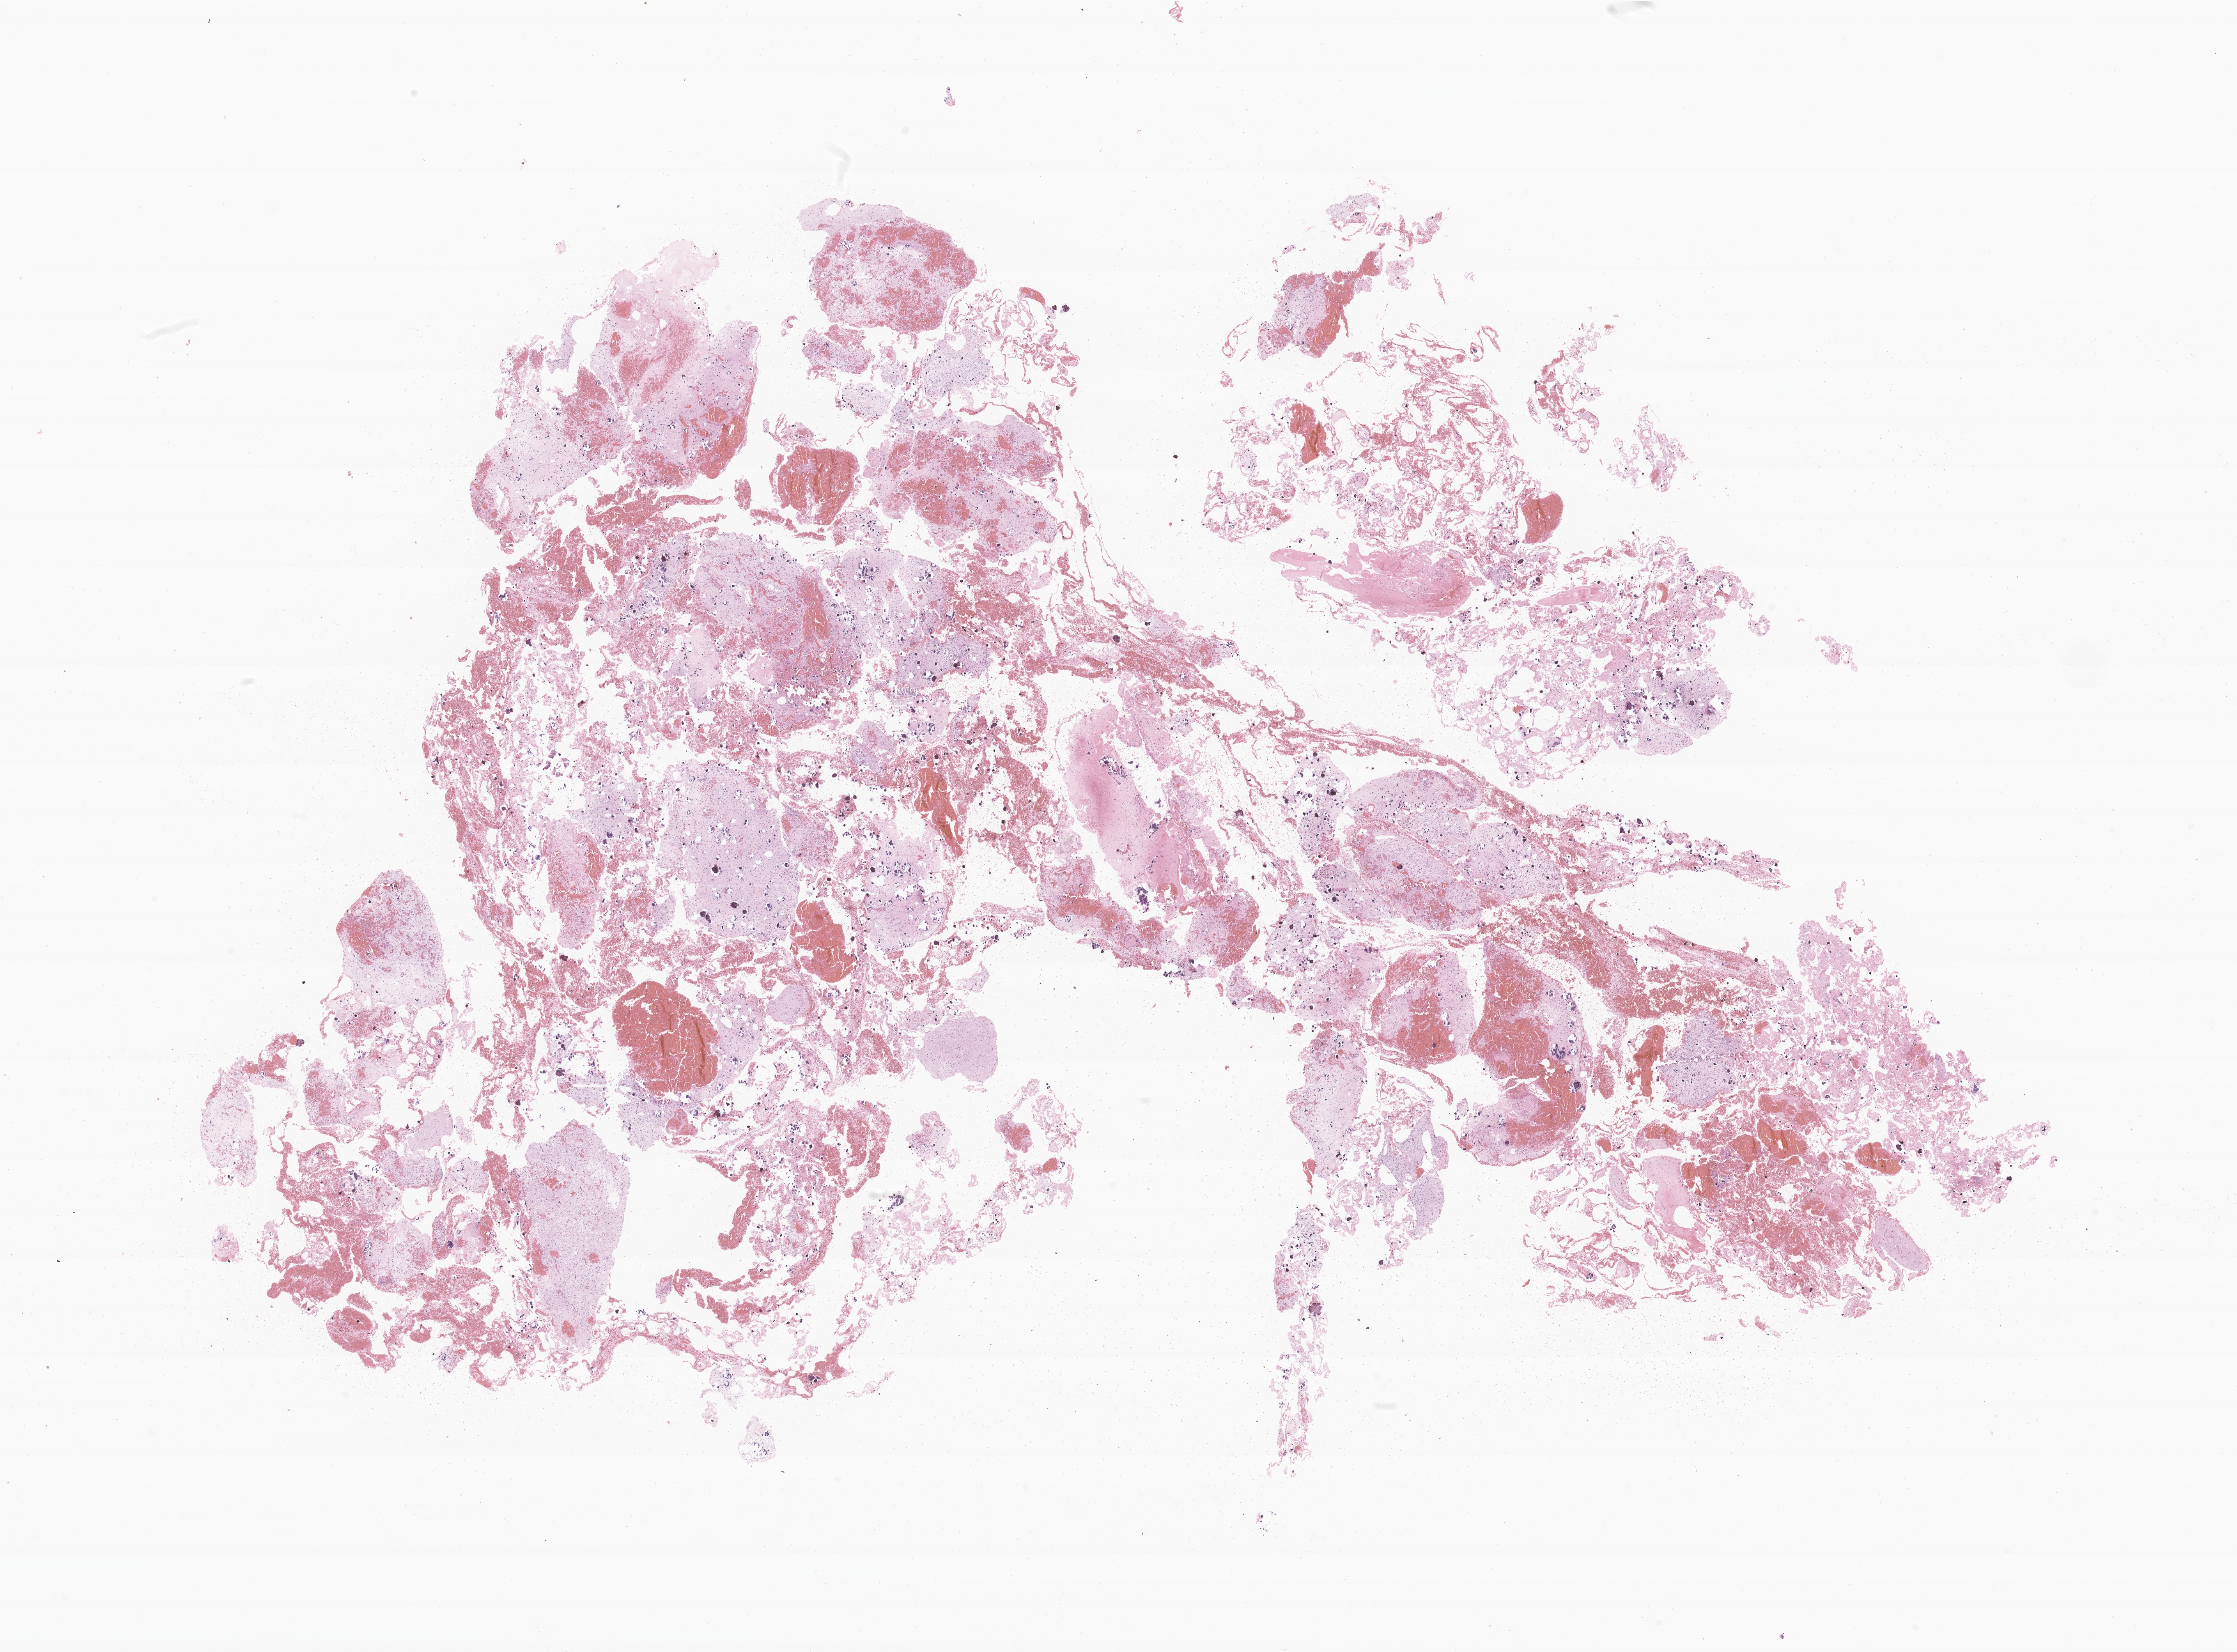
Hematoxylin and eosin (H&E) whole-slide image of tumor tissue from the frontal lobe, a low-resolution overview of the entire scanned area, about 24.1 x 17.8 mm. FFPE section. Patient: male, age 159 months (13 years 3 months).
Diagnosis: Pilocytic astrocytoma.